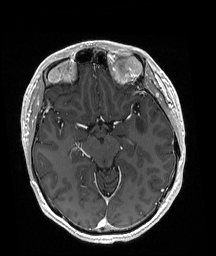
Brain MRI from a brain-tumour surgery series, one axial slice. Position 114 of 192 along the scan axis. T1-weighted post-contrast. 1 mm slice thickness. 216 × 256 image matrix. Case-level facts recorded for this patient, not image findings: histopathology: Astrocytoma; WHO grade: 3; IDH mutation: yes; tumour location: Left Posterior Frontal.
Annotated regions visible in this slice (outlined manually by an expert reader):
- tumour: bounding box (x1, y1, x2, y2) in pixels: (136, 117, 146, 137)